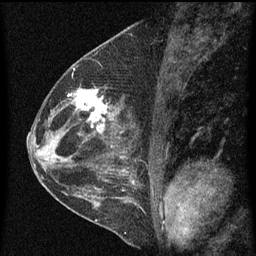
Breast MRI (dynamic contrast-enhanced), one sagittal slice; slice 29 of 60 in the series (ordered by position); dynamic contrast-enhanced series, image 2 of 4 at this slice position (ordered by acquisition); 1.5 T; TE 4.2 ms, TR 8 ms; 2 mm slice thickness; 256 × 256 image matrix. Patient: female, 48 years.
Outlined on this slice (semi-automatic segmentation, software-assisted and operator-edited):
- analysis volume of interest (the breast-tissue region the enhancement analysis was run in; not a lesion): bounding box (x1, y1, x2, y2) in pixels: (73, 86, 115, 139)
- tumour enhancement mask (voxels above the 70 % enhancement threshold inside the analysis volume of interest): (75, 88, 114, 133)